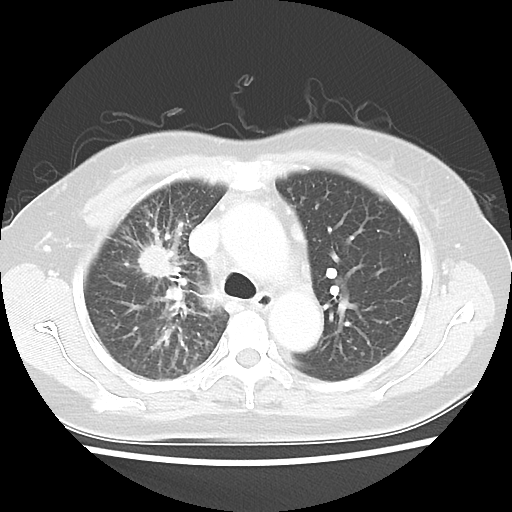
Chest CT, one axial slice. Position 31 of 48 along the scan axis. Reconstruction kernel LUNG. 100 kVp. Lung window (W 1500 / L -600 HU). 5 mm slice thickness. 512 × 512 image matrix, field of view 312 × 312 mm. Female patient, age 55 years. From the clinical record (not read from this slice): clinical TNM (as recorded): T1b N3 M1a.
Annotated regions visible in this slice (rectangle marked by the reading radiologist):
- lung tumour (recorded histology: adenocarcinoma): bounding box (x1, y1, x2, y2) in pixels: (135, 243, 184, 278)